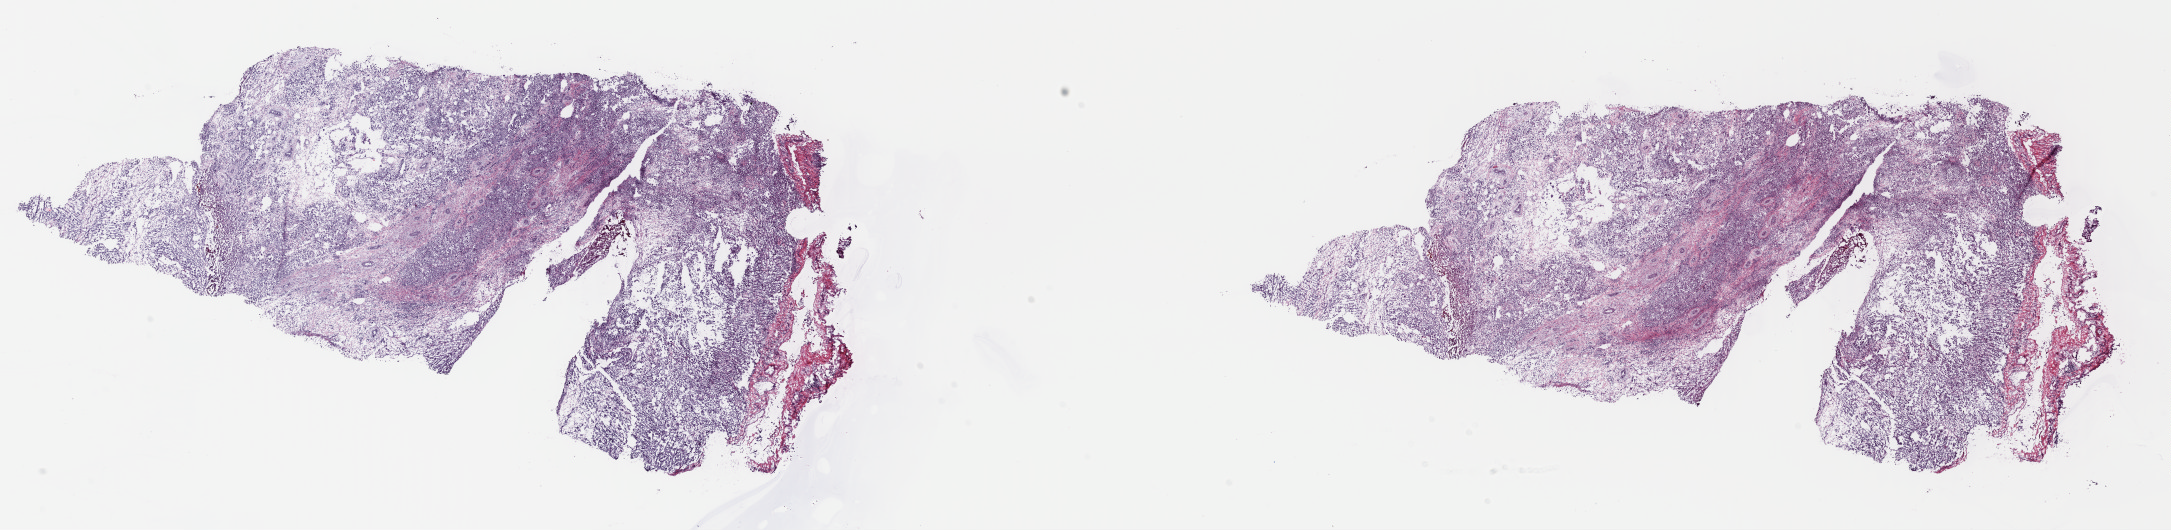
Digitized H&E-stained tissue section (whole slide) — low-resolution overview of the scanned area, about 34.1 x 8.3 mm (slide scanned at 40x), frozen section, primary tumour sample from the mesothelium. Female patient; age at initial diagnosis 60 years. Slide review estimates, as recorded: tumour cells 90%, tumour nuclei 100%, normal cells 0%, stromal cells 10%, necrosis 0%. Infiltration values recorded for this section: lymphocyte infiltration 2%, monocyte infiltration 1%, neutrophil infiltration 0%.
• histologic diagnosis: Epithelioid mesothelioma, malignant (pleura, NOS)
• AJCC pathologic stage: III
• laterality: right